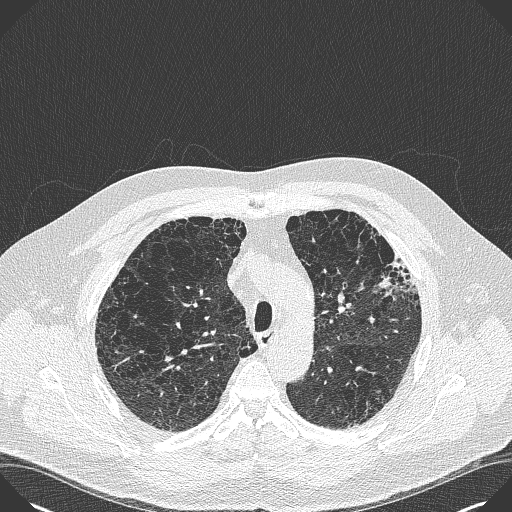
Low-dose screening chest CT, axial slice; baseline annual screen; lung window (W 1500 / L -600 HU); 512 × 512 image matrix, field of view 380 × 380 mm. Male, age 59 years at enrolment. Current smoker at enrolment.
Lesion marked by an expert reader, box from (x=373, y=250) to (x=429, y=301) px. No non-calcified nodule or mass ≥4 mm was recorded by the screening reader at this exam. Official screen result: negative screen, minor abnormalities not suspicious for lung cancer. Participant outcome: lung cancer diagnosed 909 days after this screen — bronchiolo-alveolar carcinoma, mixed mucinous and non-mucinous, left upper lobe, stage IA (AJCC 6th edition), 20 mm at pathology.